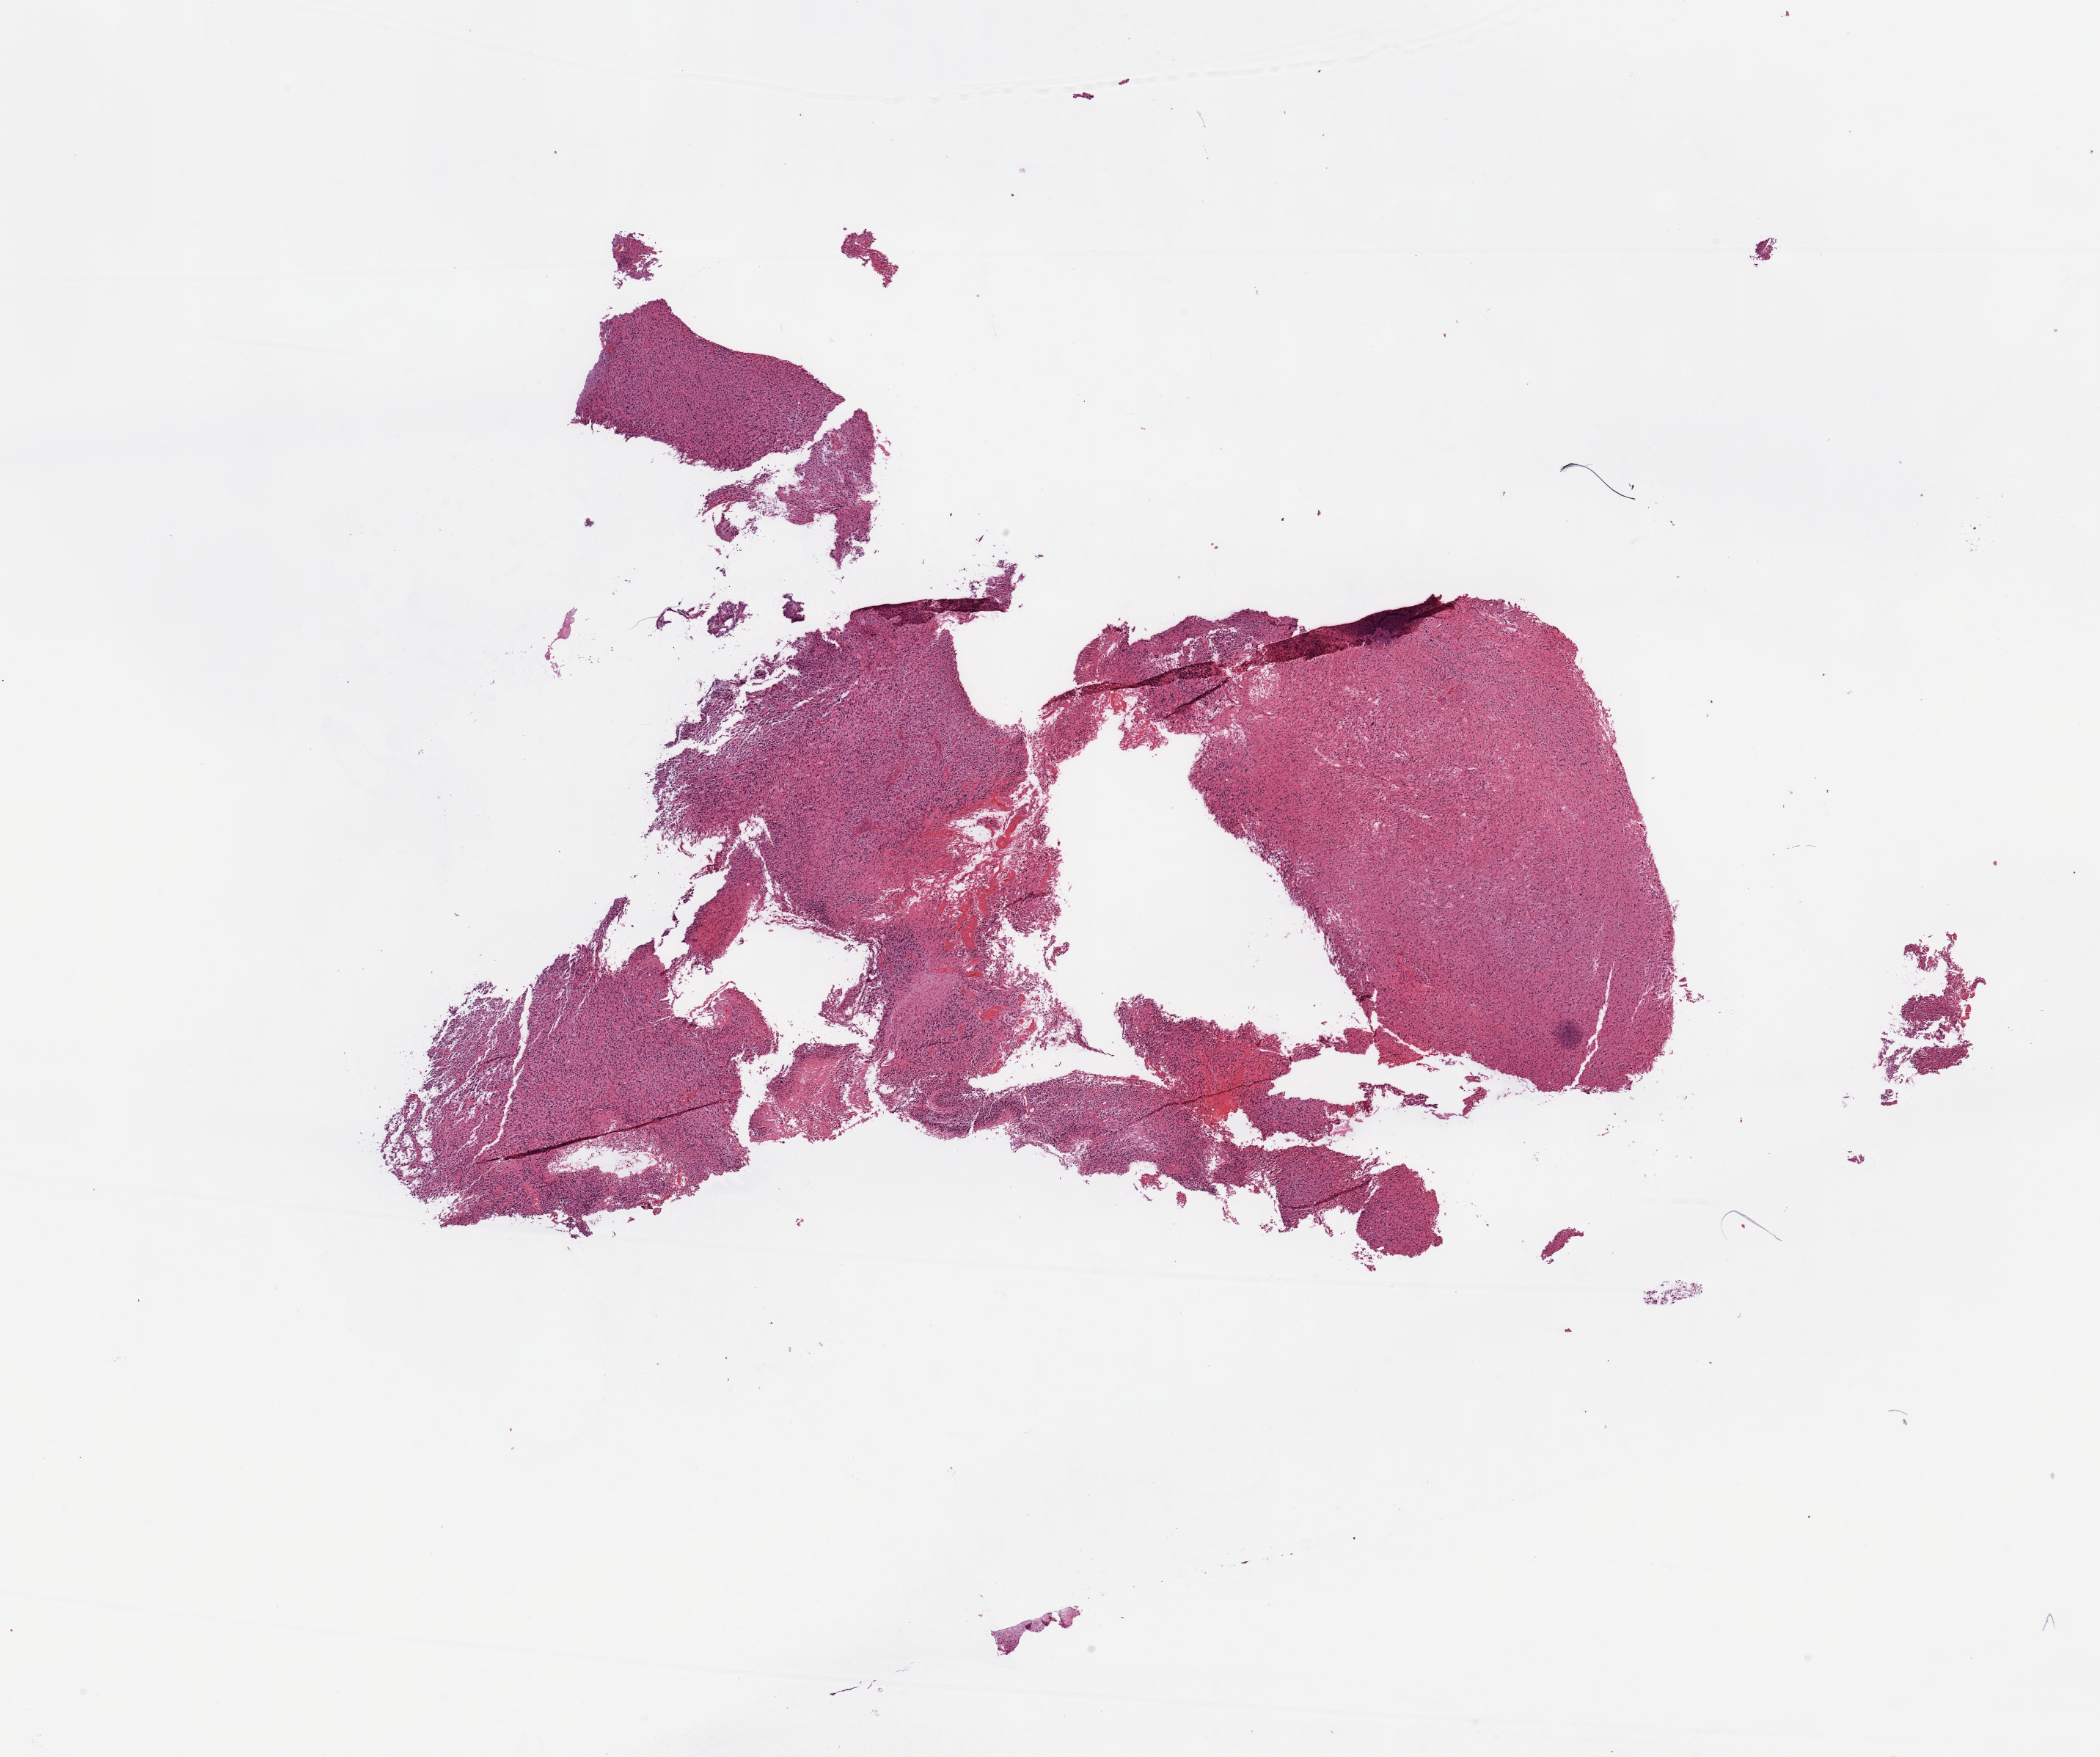
Hematoxylin and eosin (H&E) stained whole-slide image — shown as a low-resolution overview of the whole scanned area (about 22.6 x 18.9 mm); tumour tissue sample, brain. 70-year-old male patient.
• patient diagnosis (cohort enrolment): glioblastoma multiforme (brain)
• primary tumour site (as recorded): parietal lobe